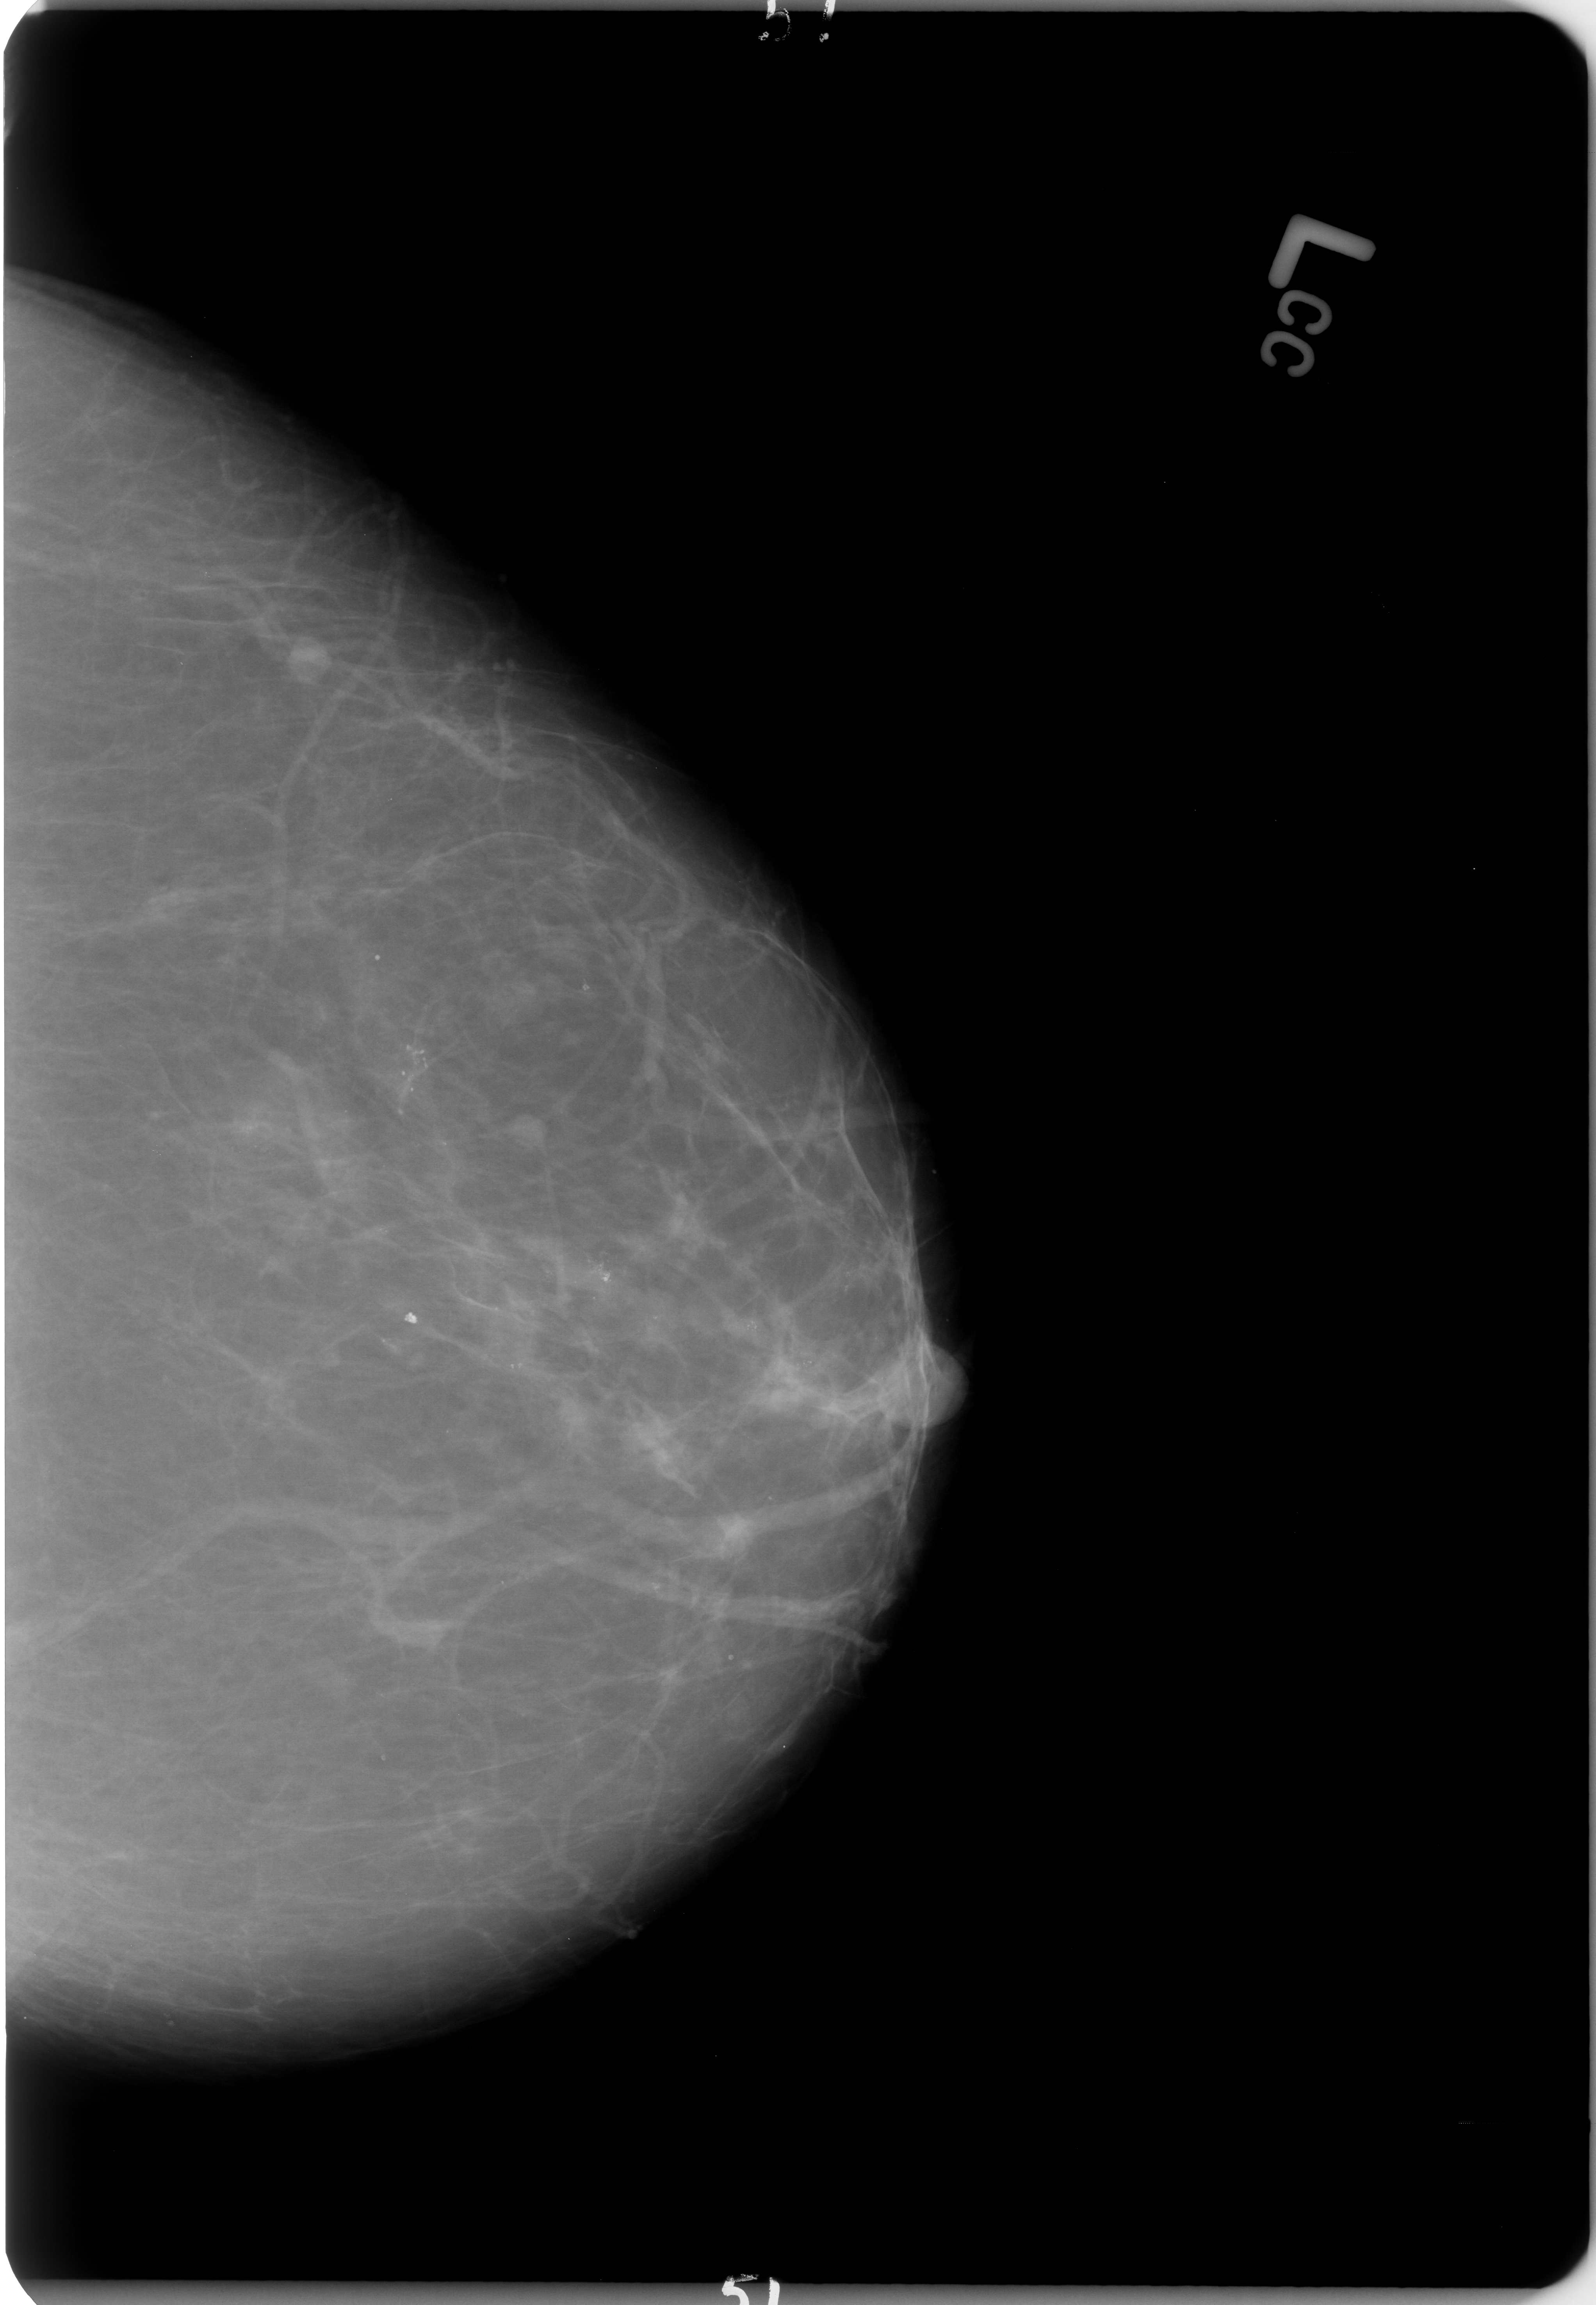
Digitized screen-film mammogram, left breast, craniocaudal (CC) view, BI-RADS breast density category 2 (scale 1–4).
Abnormality record for this image: Finding 1 of 2: calcifications, morphology pleomorphic / pleomorphic, distribution regional / regional; BI-RADS assessment category 4; pathology (as recorded): benign. Finding 2 of 2: calcifications, morphology pleomorphic, distribution regional; BI-RADS assessment category 4; subtlety rating 4 on a 1 (subtle) to 5 (obvious) scale; pathology (as recorded): benign.